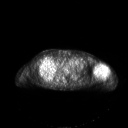
FDG PET of an extremity soft-tissue mass (from a PET/CT study), one axial slice. Position 145 of 267 along the scan axis. 3.27 mm slice thickness. 128 × 128 image matrix. Patient: female, 83 years. From the clinical record (not read from this slice): histological type: pleiomorphic leiomyosarcoma; grade: high; site of the primary tumour: left biceps.
Outlined on this slice (expert contour drawn on MRI and transferred to this co-registered scan by the dataset authors):
- gross tumour volume including surrounding oedema: bounding box [x1, y1, x2, y2] px = [94, 64, 108, 76]
- gross tumour volume (mass): [94, 64, 108, 75]